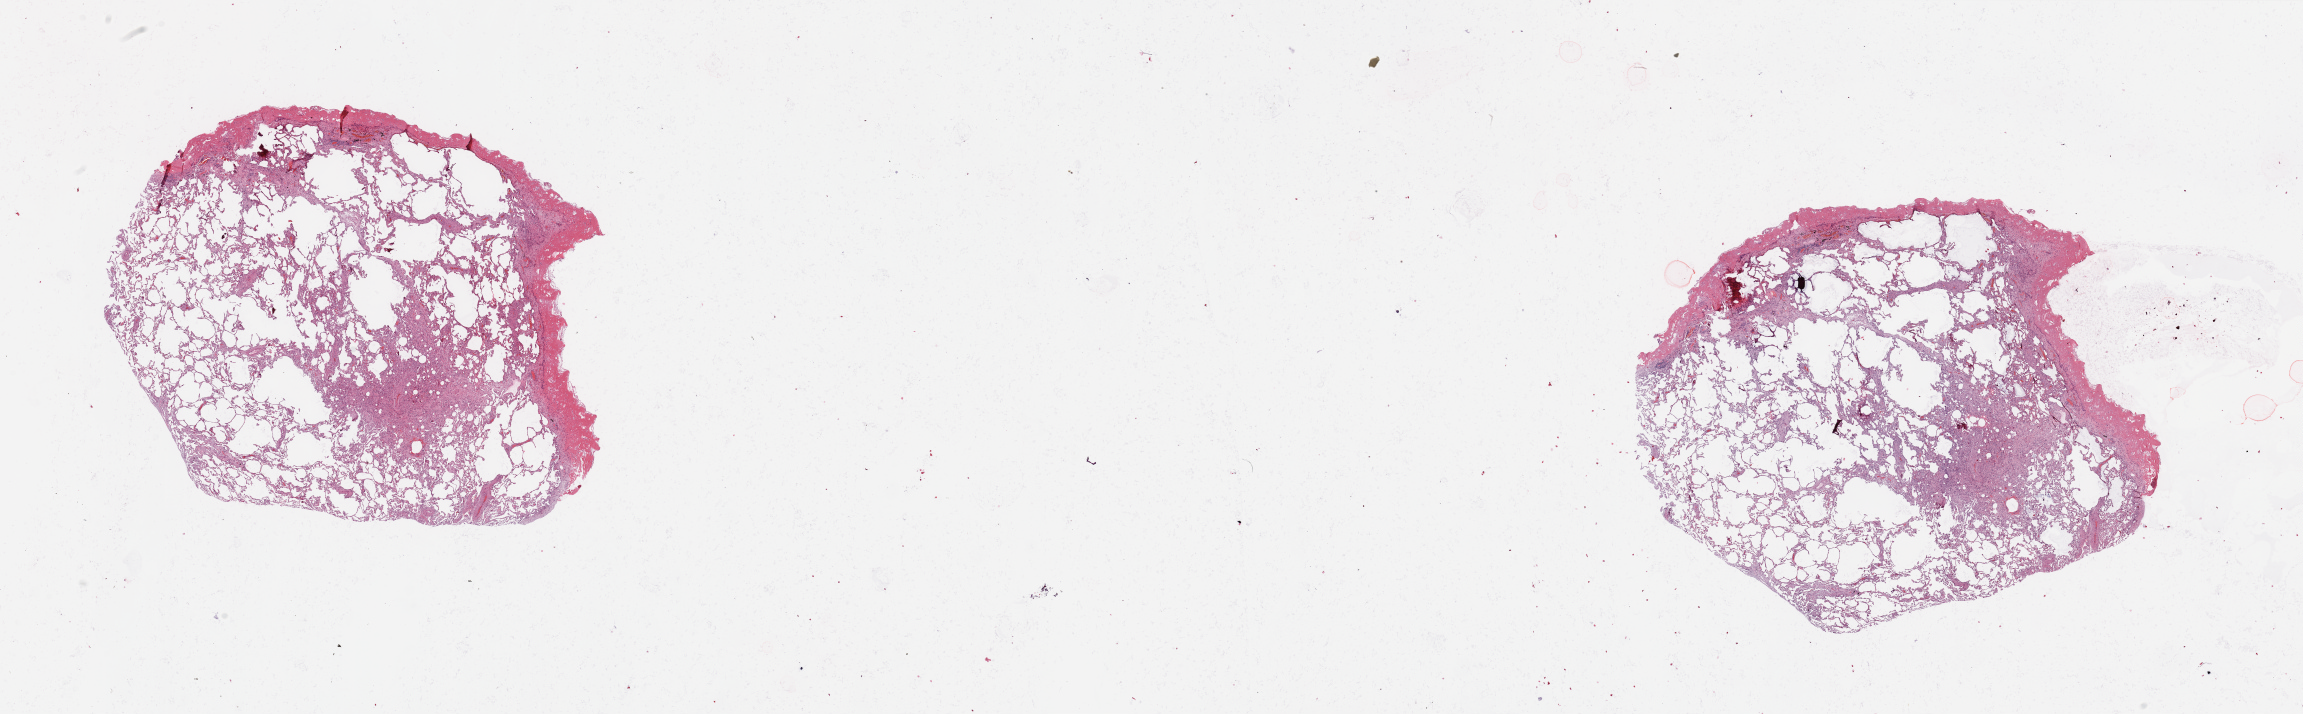
Hematoxylin and eosin (H&E) stained whole-slide image, whole scanned area (about 36.4 x 11.3 mm, slide scanned at 20x) shown as a low-resolution overview. Normal (non-tumour) tissue sample, sampled site: lung. Male, 57 y/o.
This section: normal (non-tumour) tissue from the same patient. Patient diagnosis: Squamous cell carcinoma, NOS.